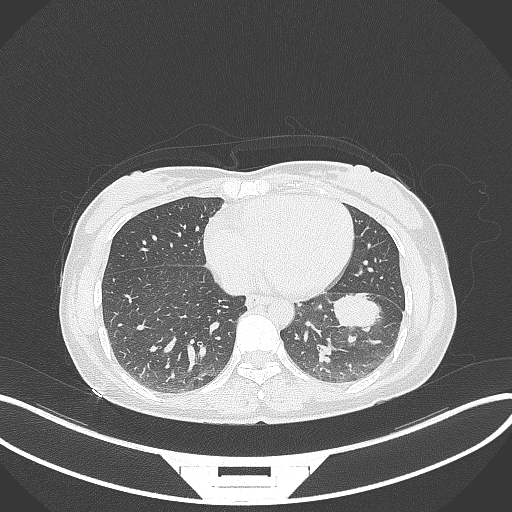
Chest CT, one axial slice. Slice 12 of 244 in the series (ordered by position). Reconstruction kernel B70f. Lung window (W 1500 / L -600 HU). 1 mm slice thickness. 512 × 512 image matrix, field of view 400 × 400 mm. Patient: female, 41 years. From the clinical record (not read from this slice): clinical TNM (as recorded): T2a N3 M1b.
Structures marked on this image (bounding box drawn by a radiologist):
- lung tumour (recorded histology: adenocarcinoma): bounding box [x1, y1, x2, y2] px = [333, 291, 389, 332]